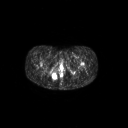
FDG PET of an extremity soft-tissue mass (from a PET/CT study), one axial slice. Slice 32 of 267 in the series (ordered by position). 3.27 mm slice thickness. 128 × 128 image matrix. Patient: female, 17 years. From the clinical record (not read from this slice): histological type: epithelioid sarcoma; grade: intermediate; site of the primary tumour: right buttock.
Structures marked on this image (expert contour drawn on MRI and transferred to this co-registered scan by the dataset authors):
- gross tumour volume including surrounding oedema: bounding box (x1, y1, x2, y2) in pixels: (50, 71, 58, 81)
- gross tumour volume (mass): (50, 72, 57, 80)